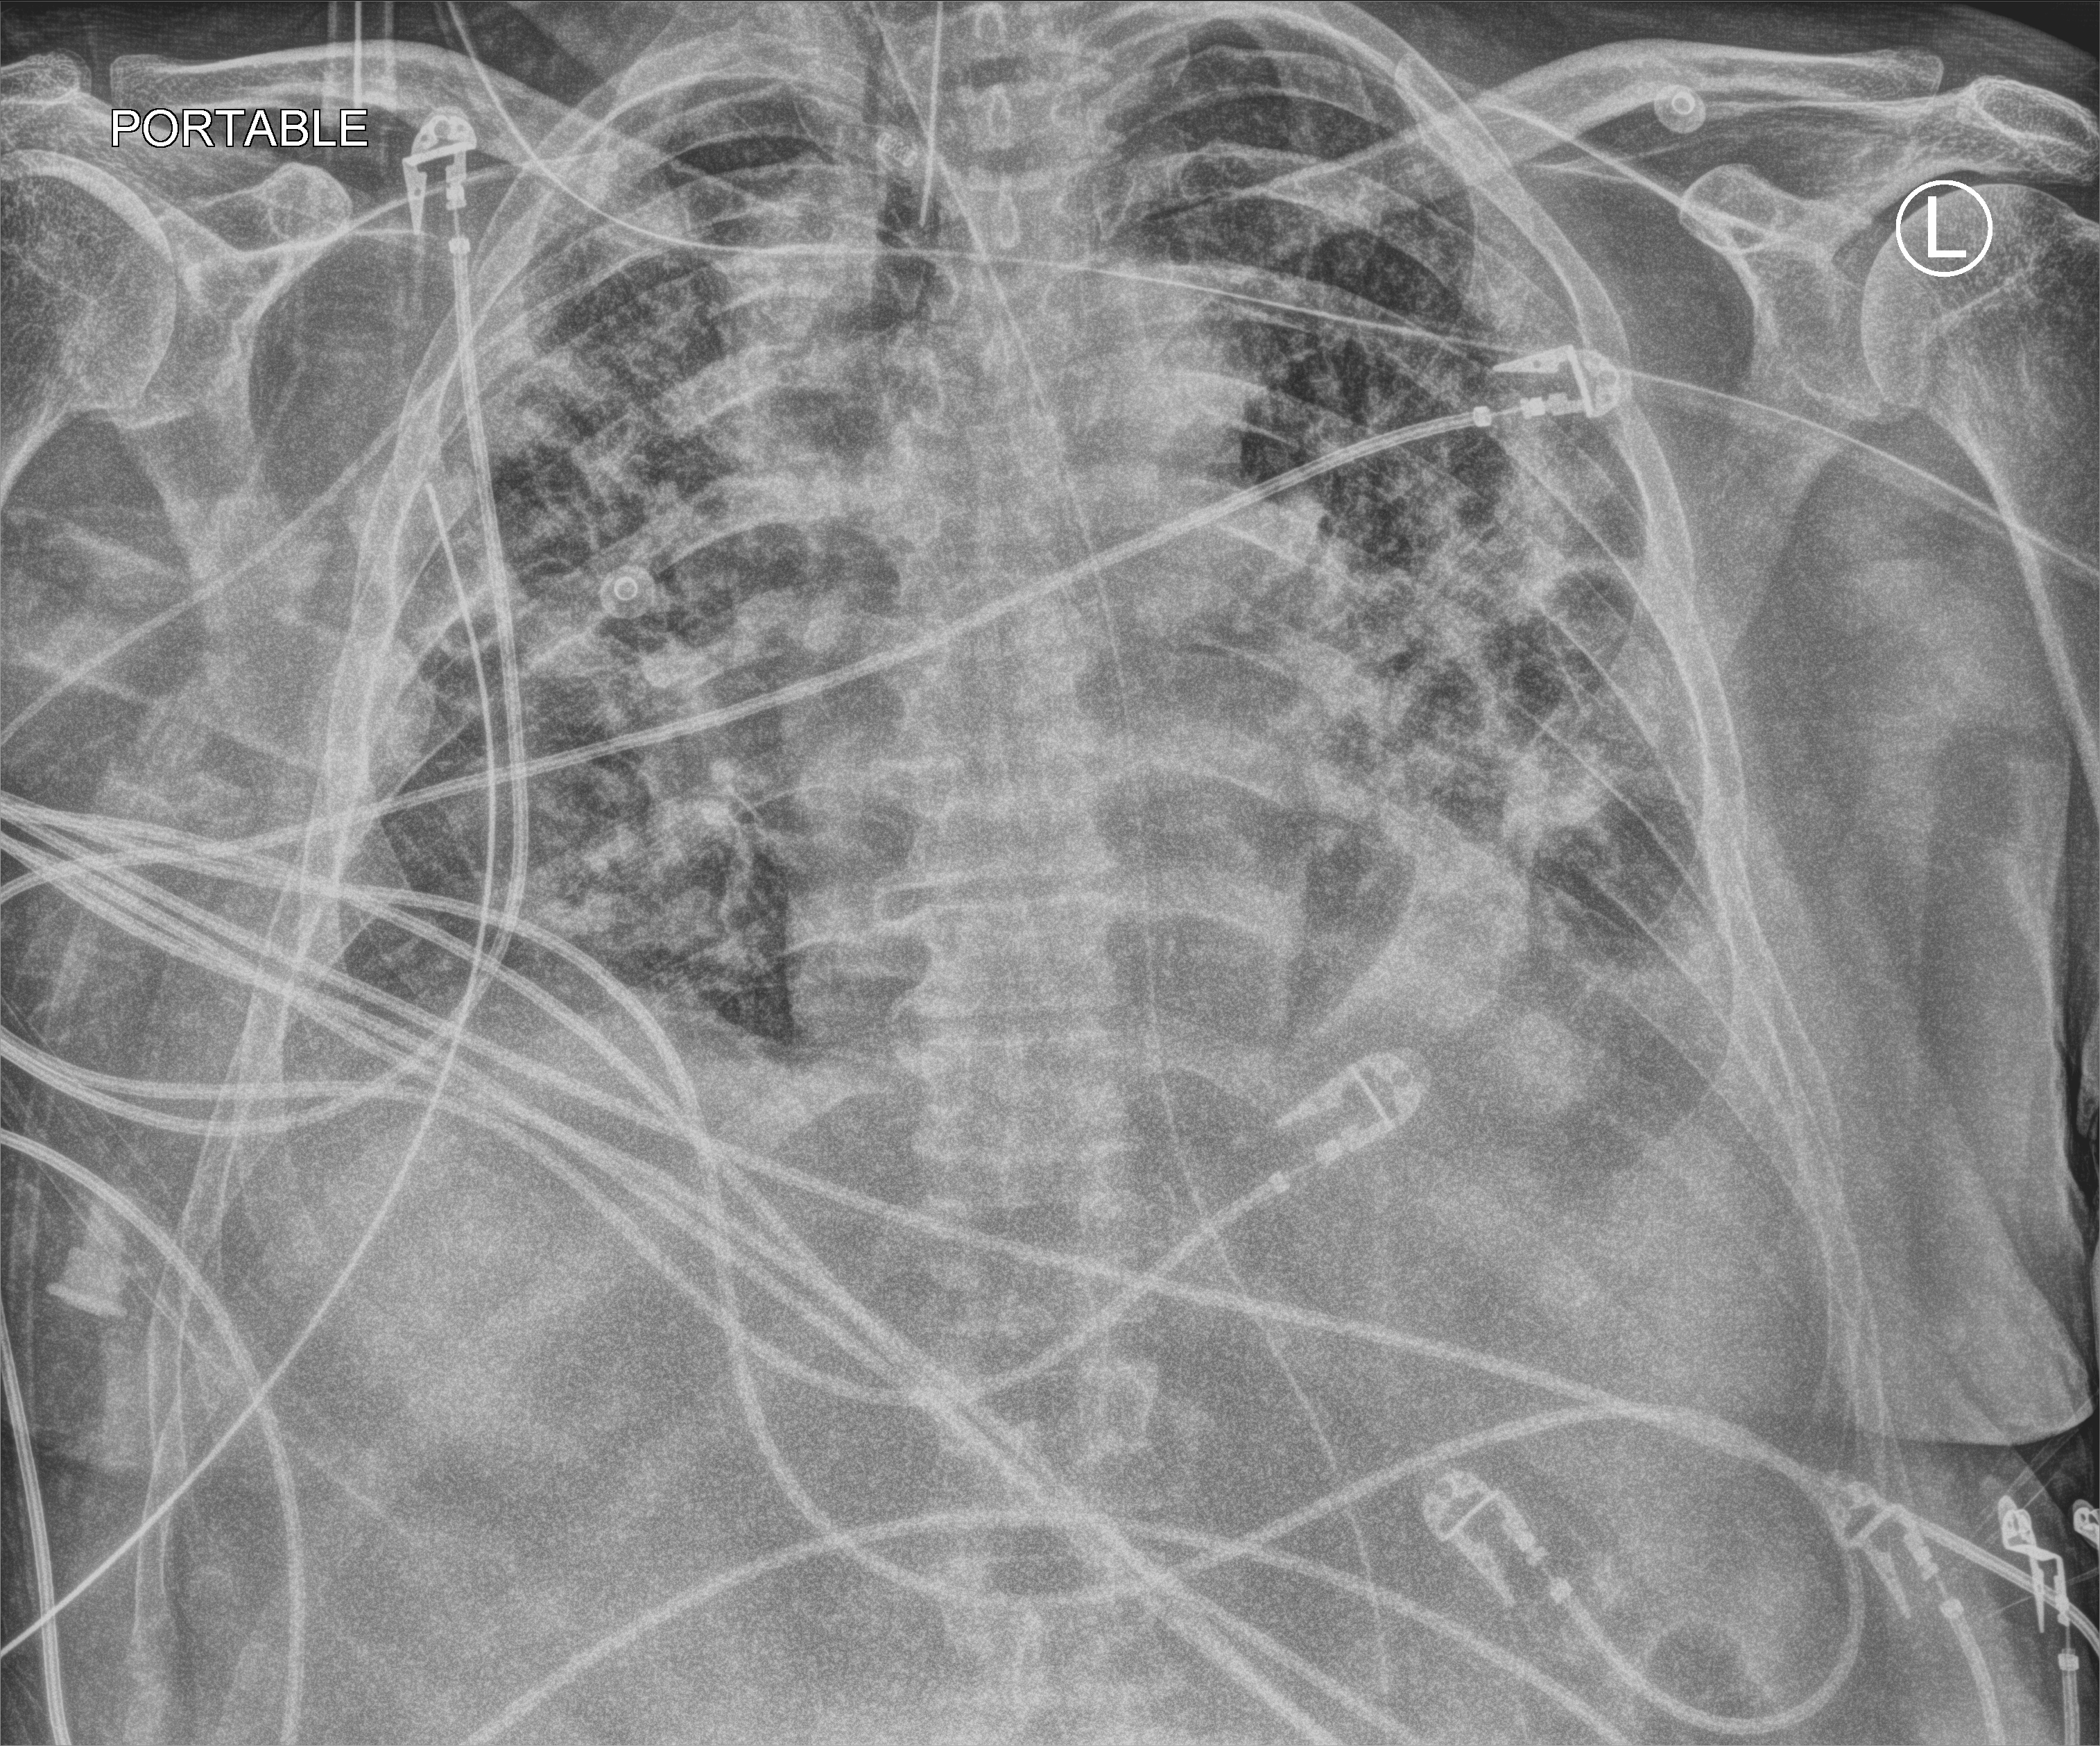
Bedside chest radiograph (computed radiography); anteroposterior (AP) projection. Patient hospitalised with COVID-19; male, aged 60–74 years.
Hospital-stay facts (about this admission, not read from this image; timing relative to this image not recorded): hypertension (admission record): no; COPD (admission record): no; admitted to intensive care during this hospital stay: yes.